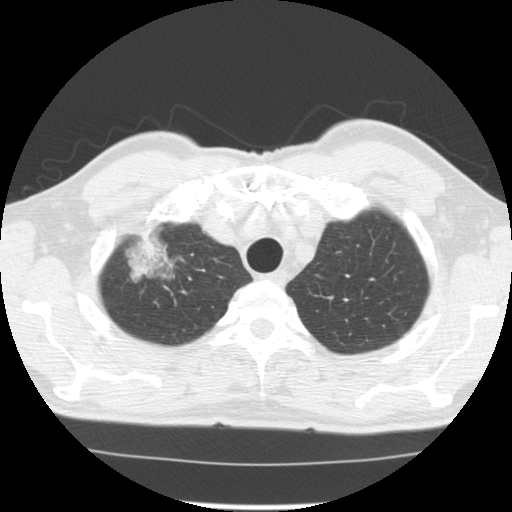
Low-dose screening chest CT, one axial slice. Position 108 of 128 along the scan axis. 120 kVp. Lung window (W 1500 / L -600 HU). 512 × 512 image matrix, field of view 340 × 340 mm.
Structures marked on this image (manually delineated by an expert):
- lesion 1 (tumor, upper lobe of right lung): bounding box (x1, y1, x2, y2) in pixels: (134, 238, 169, 268)